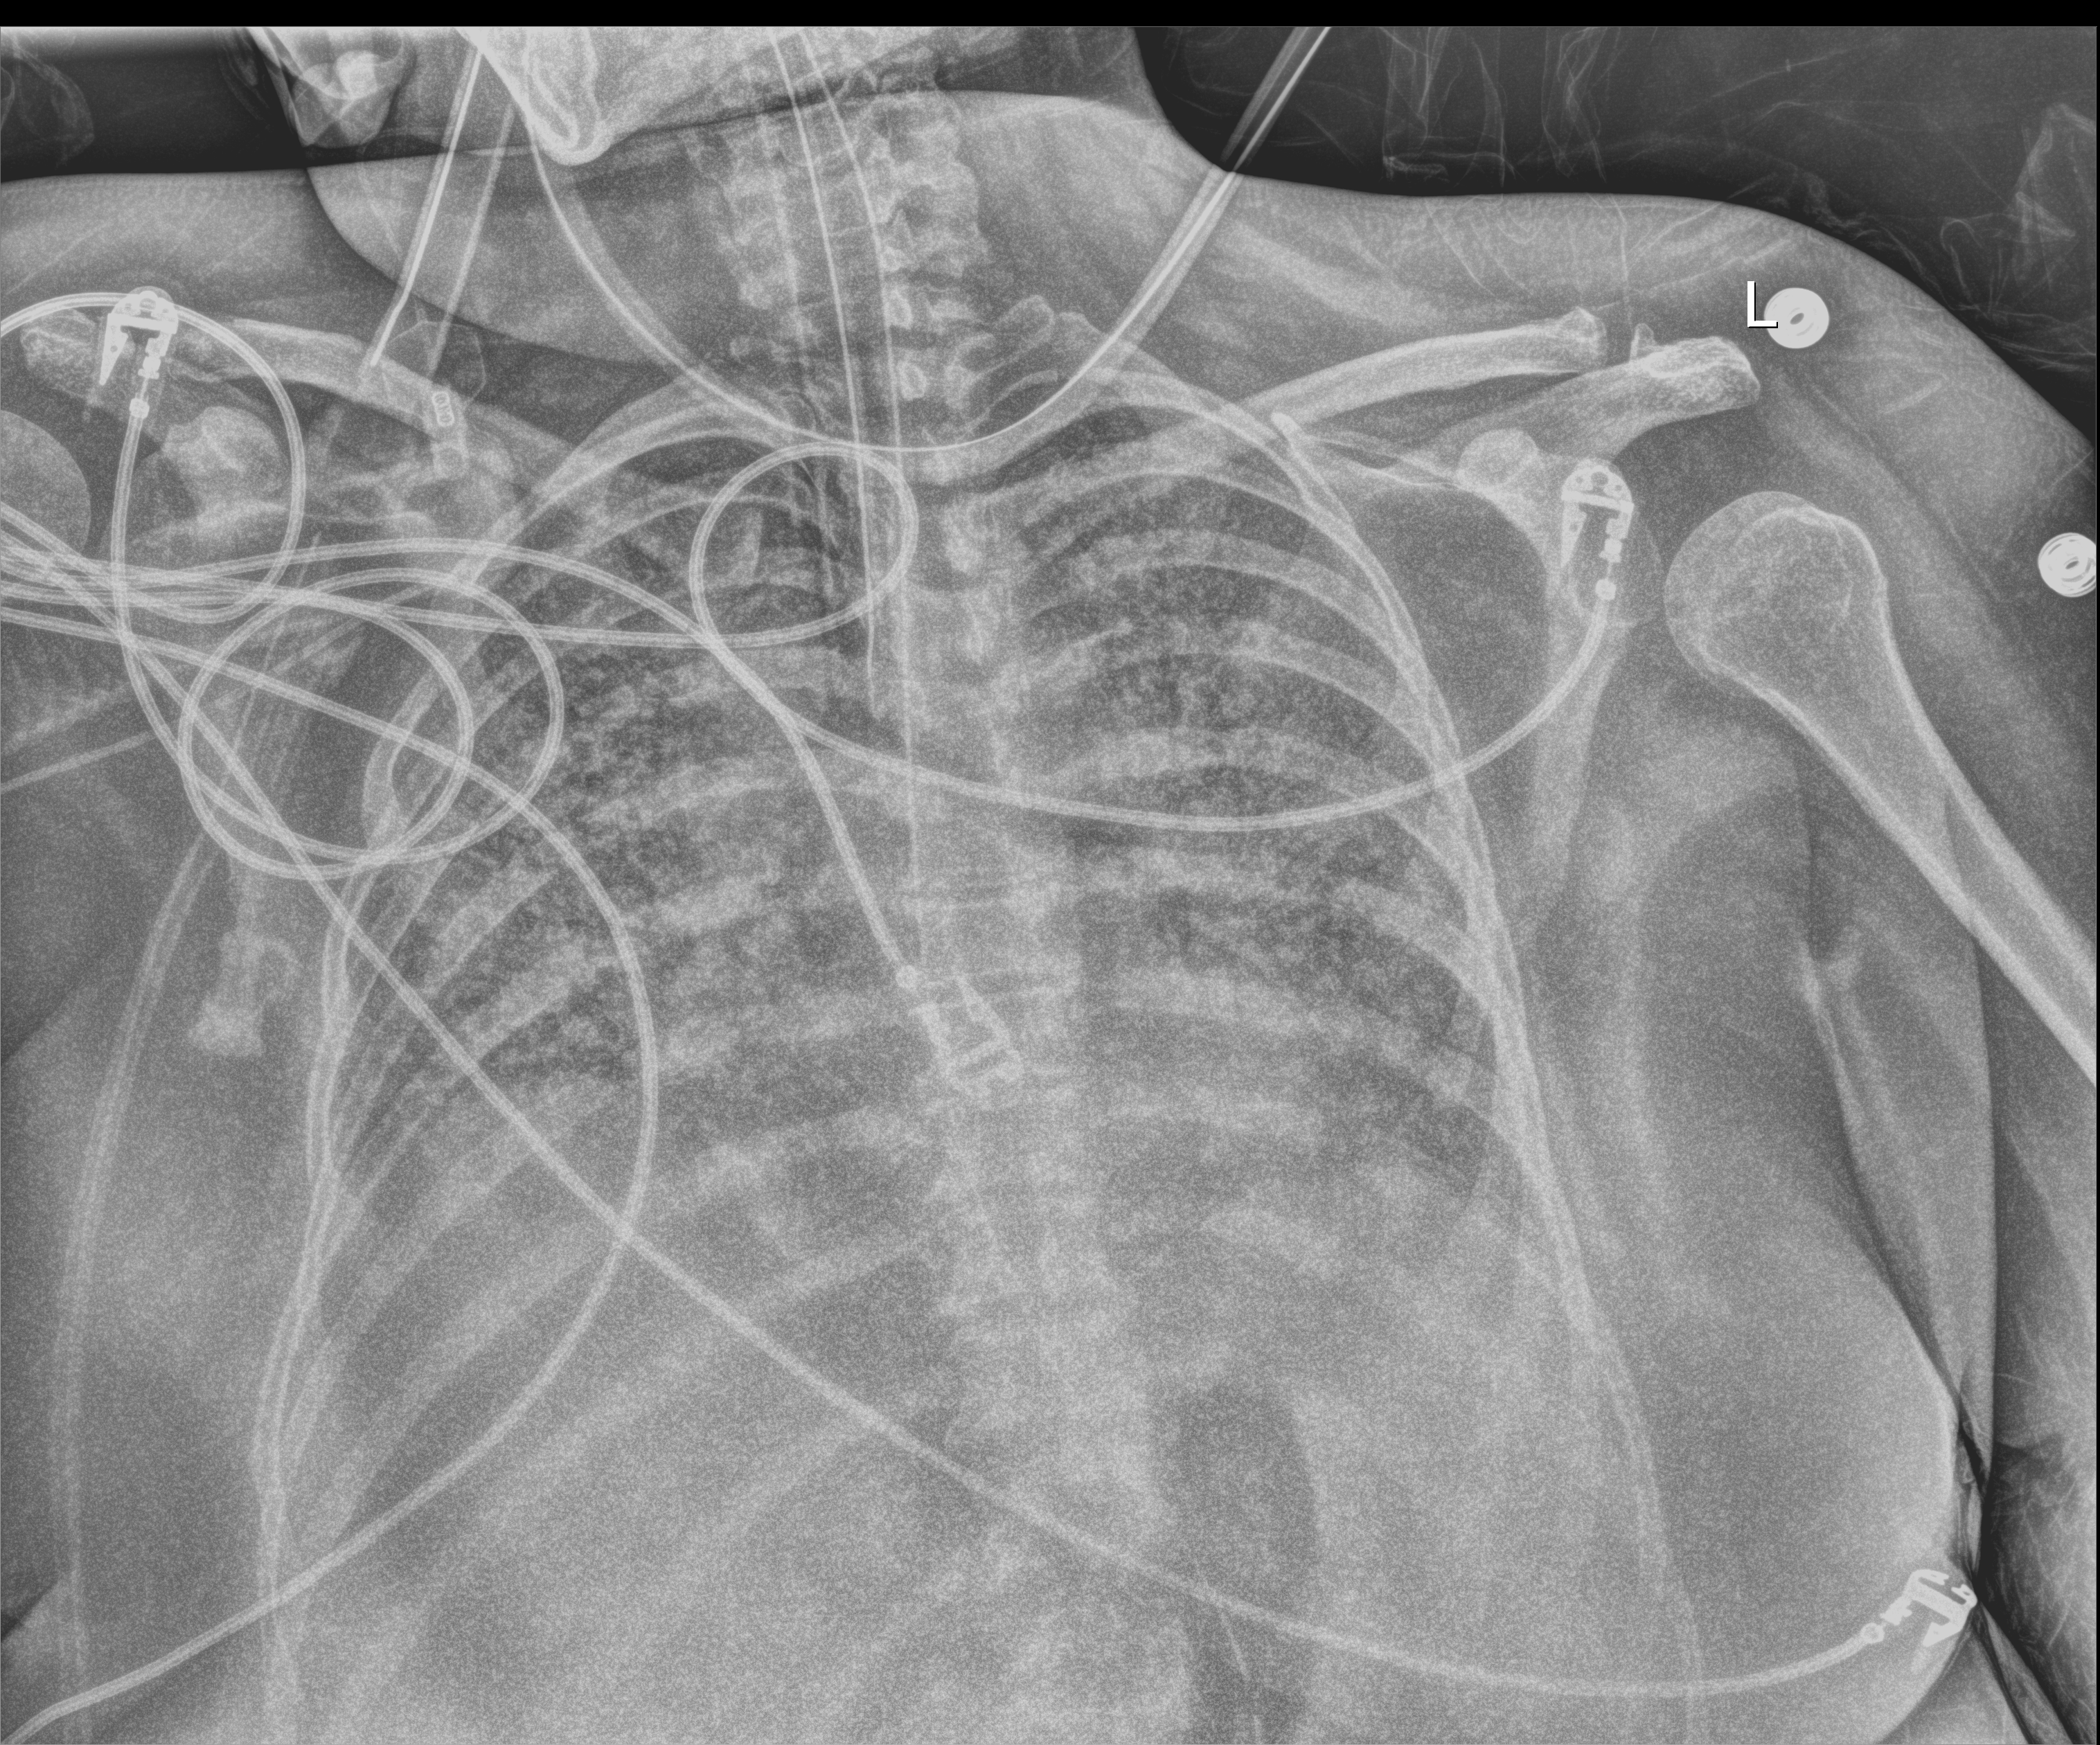
Portable chest radiograph; anteroposterior (AP) projection. Female patient hospitalised with COVID-19, age 18–59 years.
Hospital-stay facts (about this admission, not read from this image; timing relative to this image not recorded): admitted to intensive care during this hospital stay: yes; length of hospital stay: 95 days.